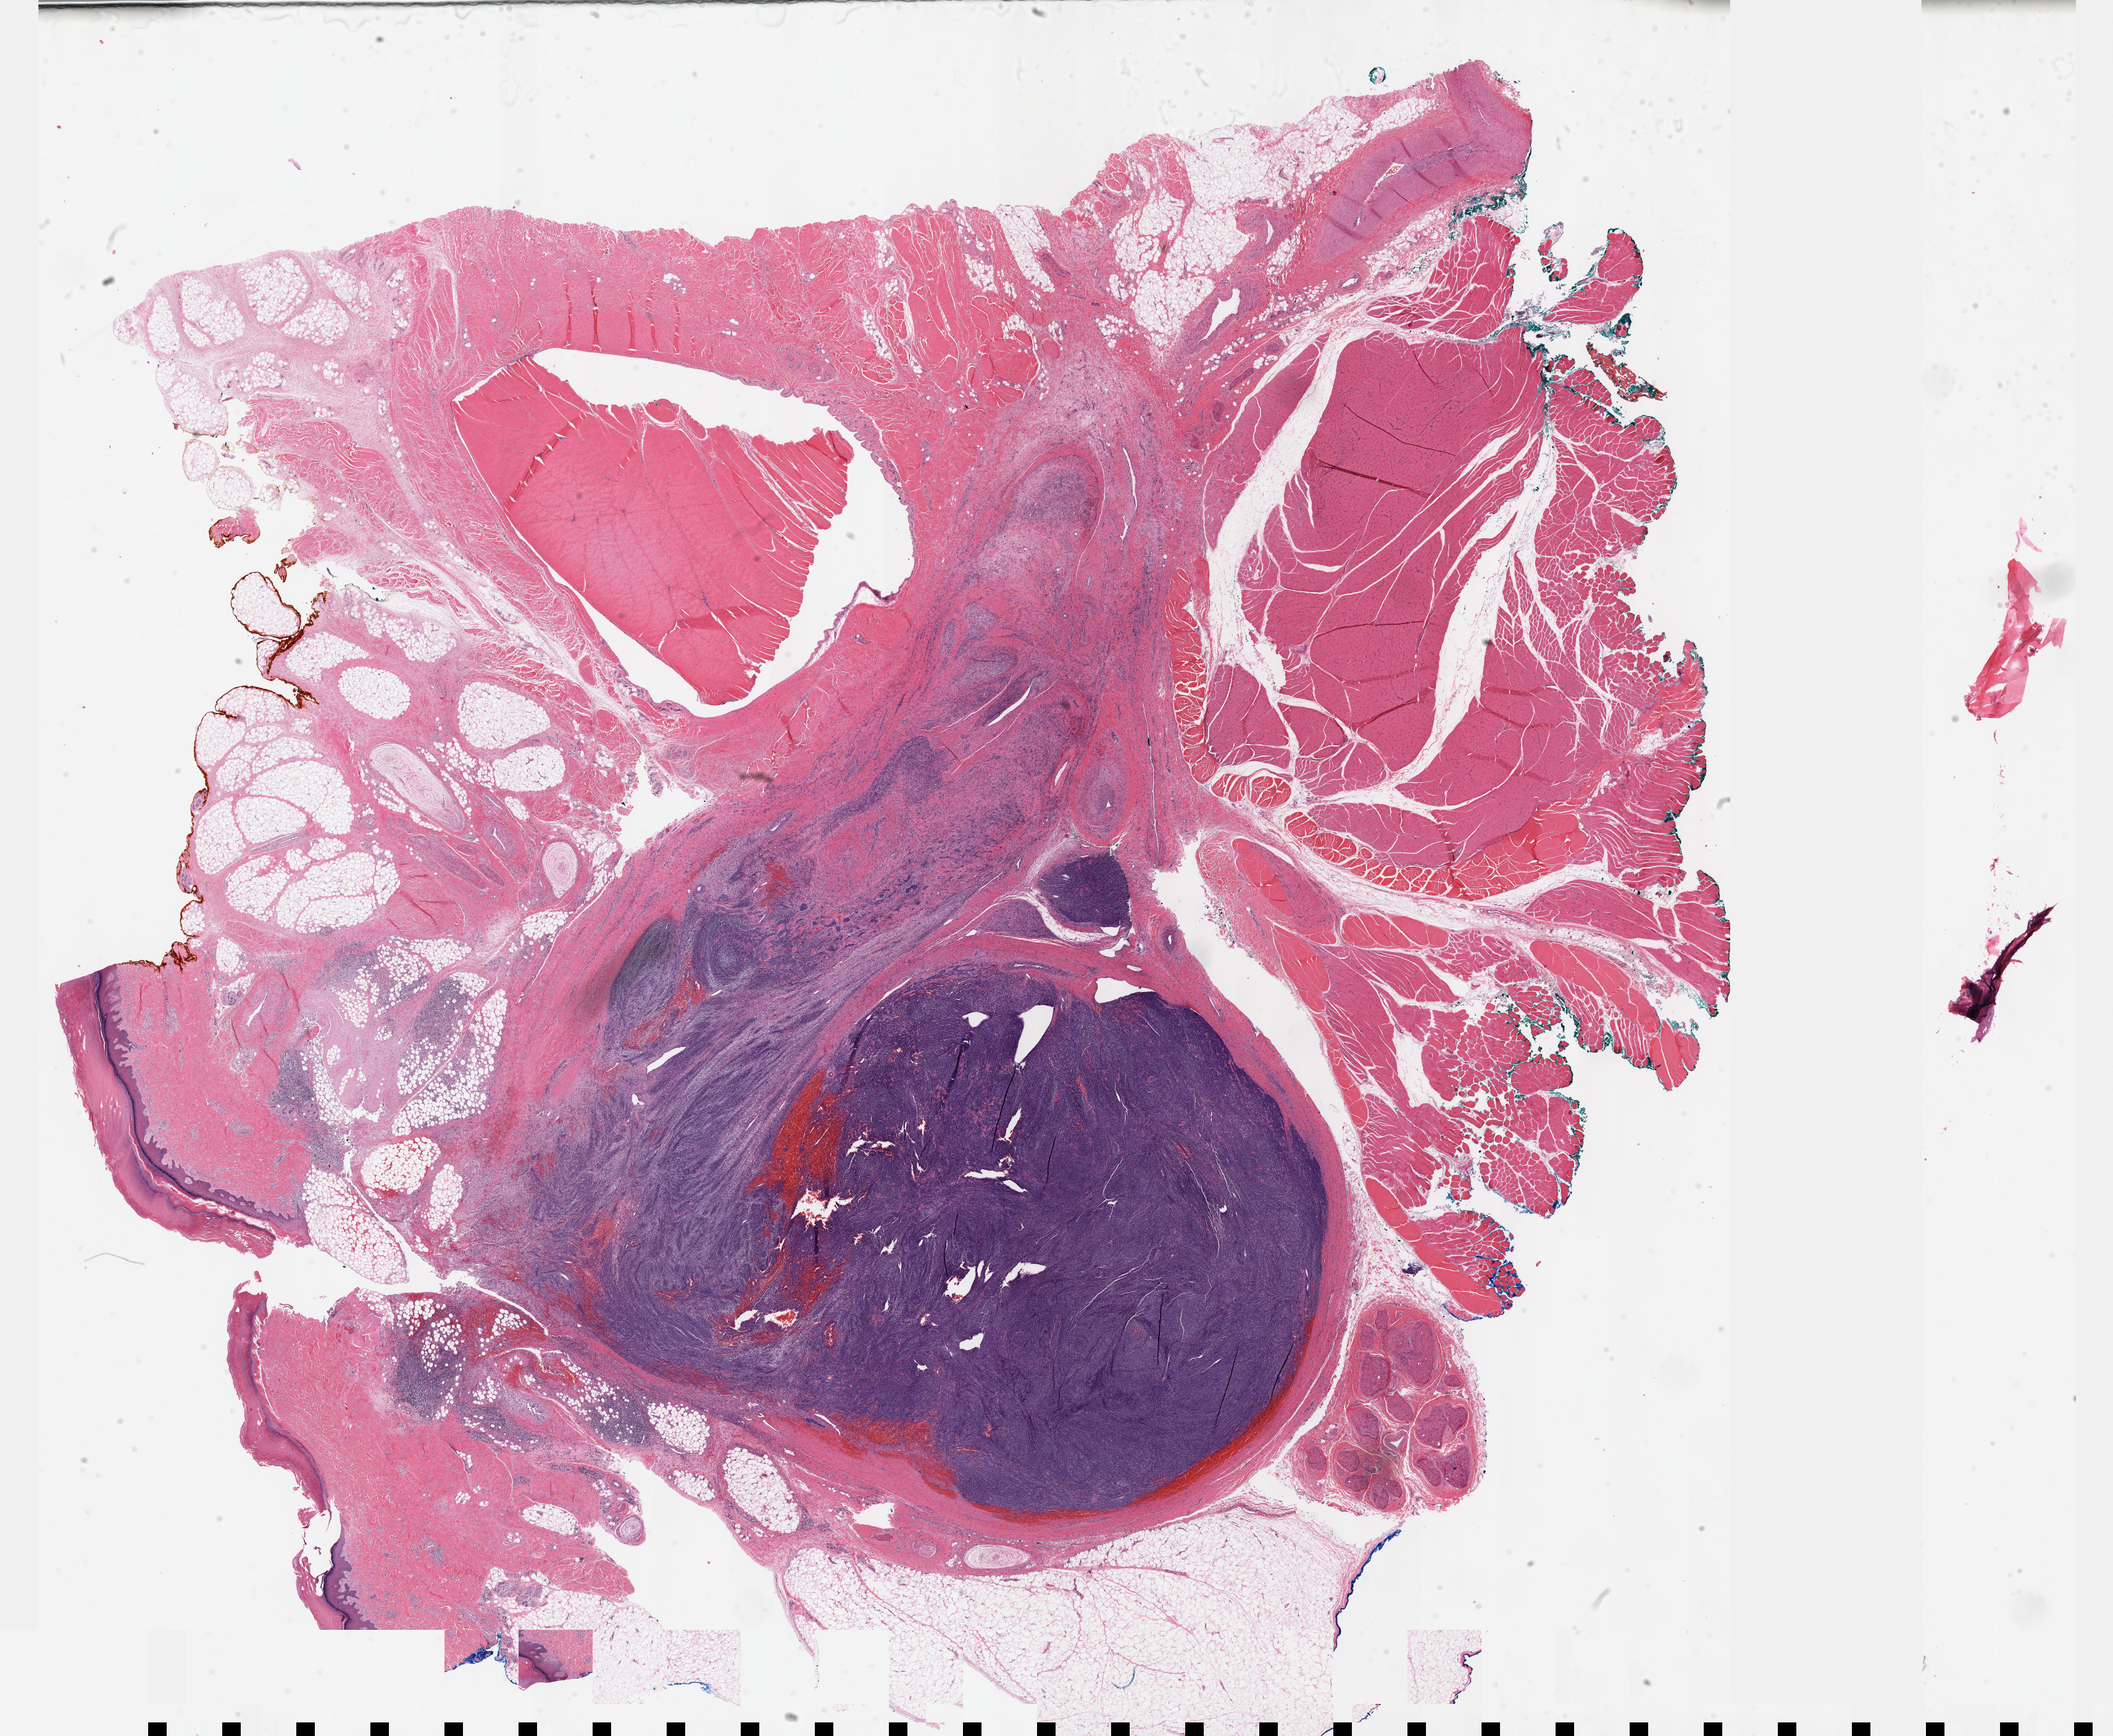
H&E whole-slide image — a low-resolution overview of the entire scanned area, about 27.7 x 22.7 mm (acquisition: 40x scan), formalin-fixed paraffin-embedded (FFPE) diagnostic section, sample: primary tumour, connective, subcutaneous and other soft tissues. Female patient; age at initial diagnosis 24 years.
Diagnosis: Synovial sarcoma, biphasic (connective, subcutaneous and other soft tissues of lower limb and hip).